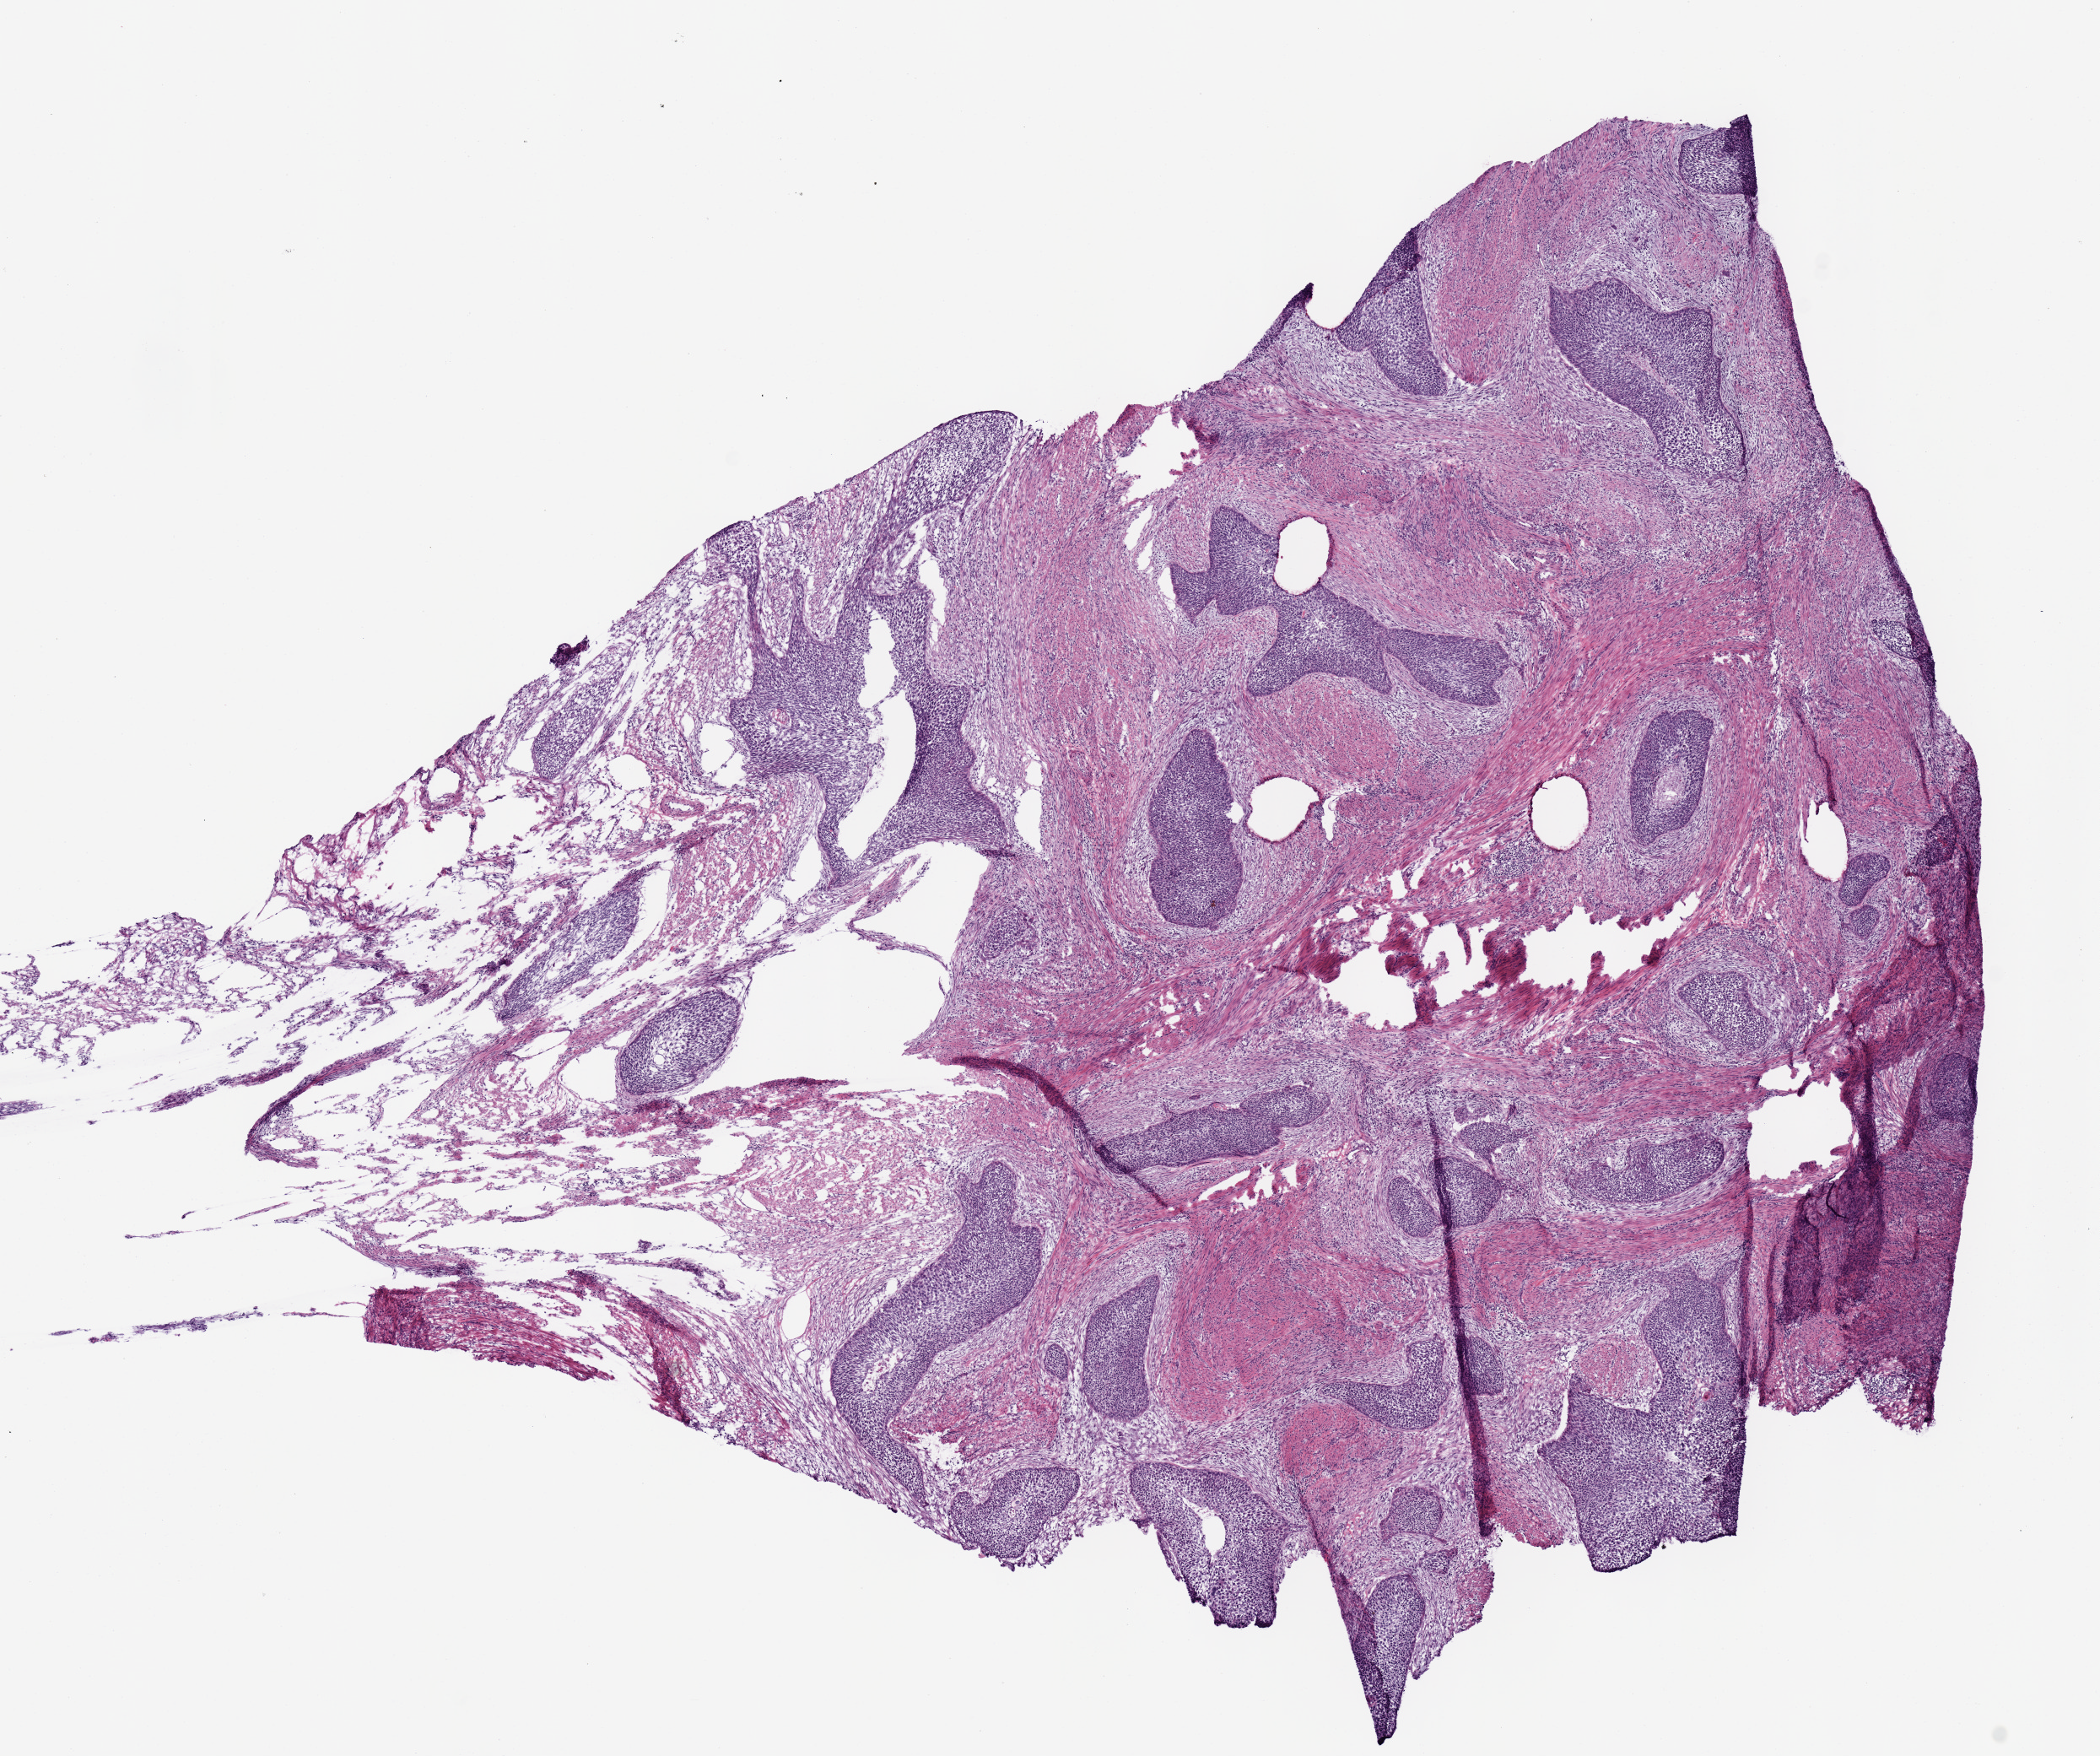
Digitized H&E tissue section (whole slide), low-resolution overview of the scanned area, about 9.8 x 8.2 mm (slide scanned at 20x). Frozen section from the top of the tissue portion. Cervix, primary tumour sample. Female patient; age at initial diagnosis 64 years. Histologic grade: G3 (poorly differentiated). Composition of this section per pathologist review: tumour cells 75%, tumour nuclei 65%, normal cells 0%, stromal cells 25%, necrosis 0%. Infiltration values recorded for this section: lymphocyte infiltration 0%, monocyte infiltration 0%, neutrophil infiltration 0%.
Pathologic diagnosis: Squamous cell carcinoma, NOS (cervix uteri). FIGO stage: IIA2.